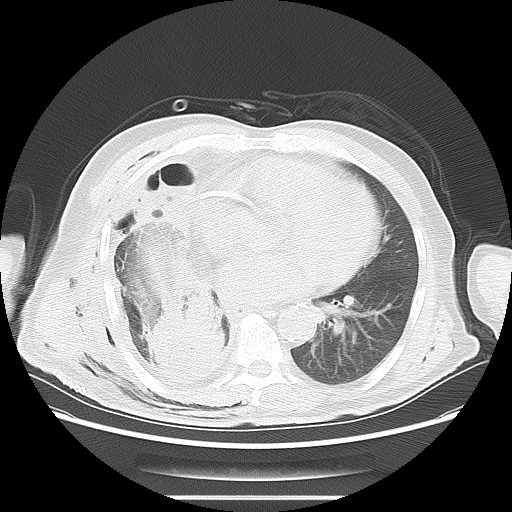
Chest CT, one axial slice. Position 28 of 59 along the scan axis. Reconstruction kernel LUNG. 120 kVp. Lung window (W 1500 / L -600 HU). 5 mm slice thickness. 512 × 512 image matrix, field of view 392 × 392 mm. Patient: male, 69 years. Case-level facts recorded for this patient, not image findings: clinical TNM (as recorded): T3 N0 M0; histopathological grade: G2-3.
Outlined on this slice (rectangle marked by the reading radiologist):
- lung tumour (recorded histology: squamous cell carcinoma): bounding box <145,296,242,386> (left, top, right, bottom; pixels)